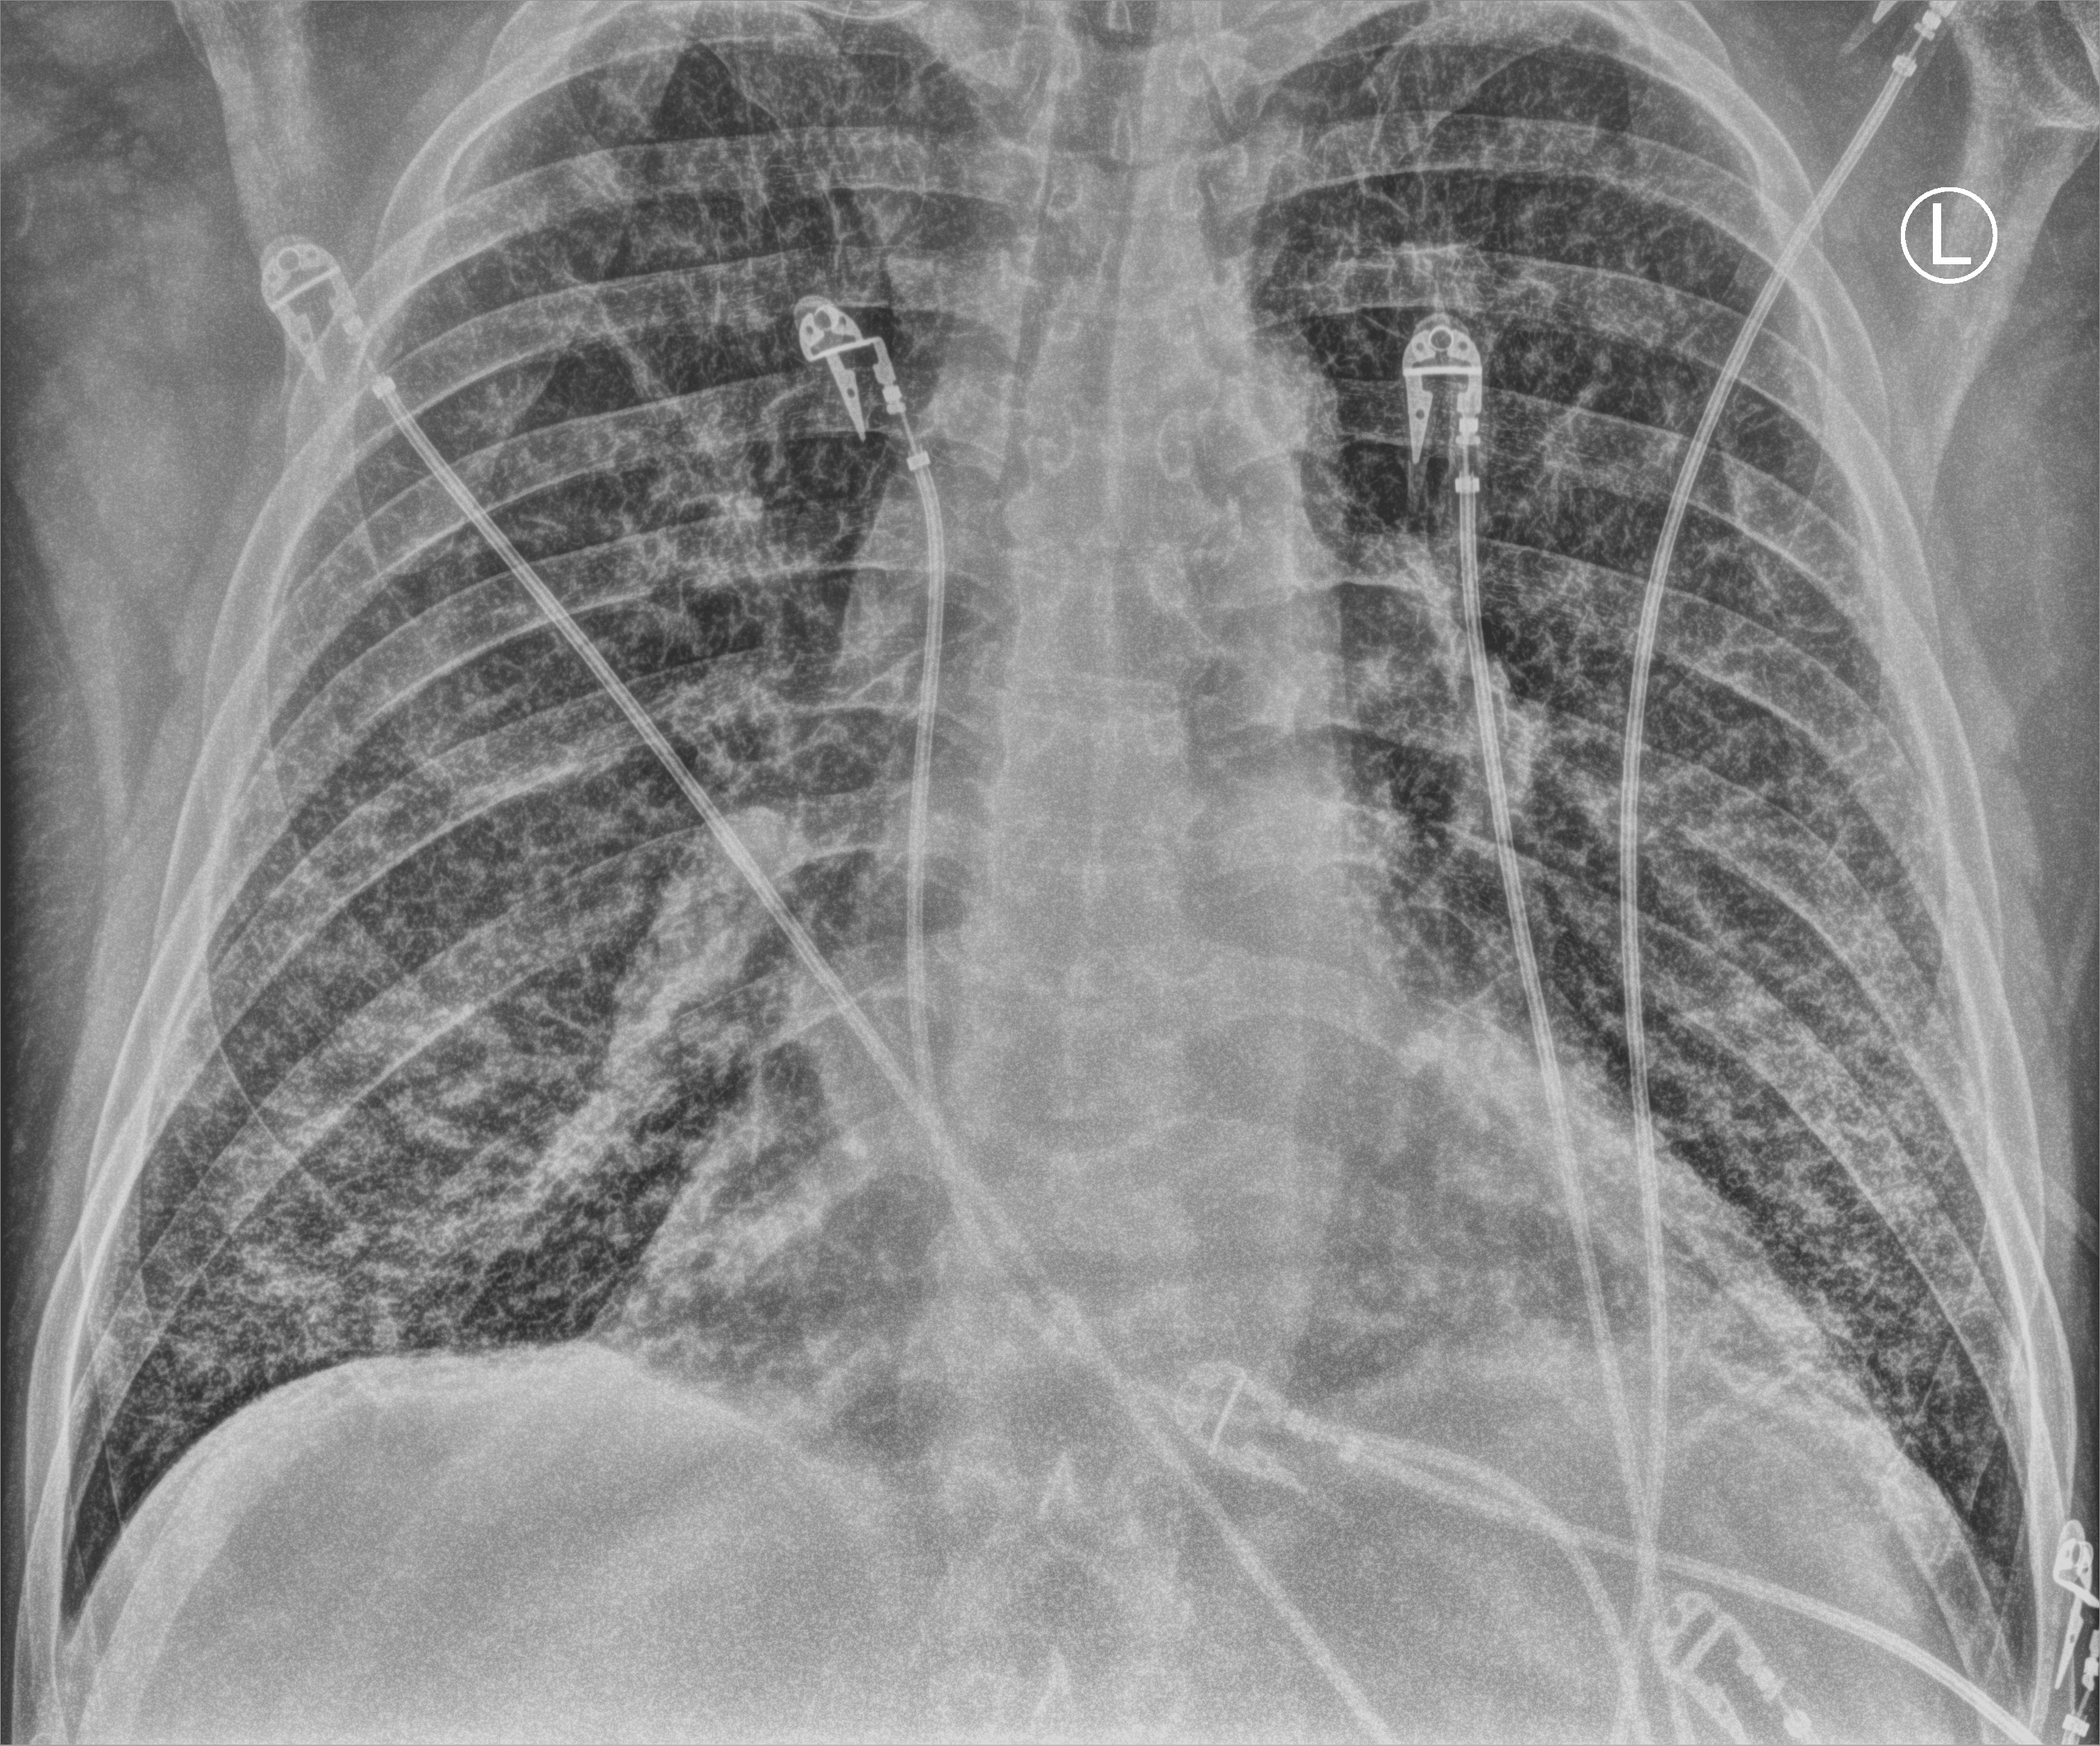
Portable chest radiograph; anteroposterior (AP) projection. Adult patient hospitalised with COVID-19, age 18–59 years.
From the hospital-stay record, not from the radiograph (when in the stay this image was taken is not recorded):
- length of hospital stay: 3 days